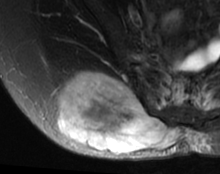
MRI of an extremity soft-tissue mass, one axial slice; slice 33 of 63 in the series (ordered by position); T2-weighted fat-saturated; MR volume resampled by the dataset authors to the PET/CT grid (not the native acquisition matrix); 3.27 mm slice thickness; 220 × 174 image matrix, field of view 215 × 170 mm. Female patient. Case-level facts recorded for this patient, not image findings: histological type: spindle cell suggestive of myxofibrosarcoma; grade: intermediate; site of the primary tumour: right buttock.
Annotated regions visible in this slice (expert contour drawn on MRI and transferred to this co-registered scan by the dataset authors):
- gross tumour volume (mass): box from (x=56, y=72) to (x=183, y=156) px